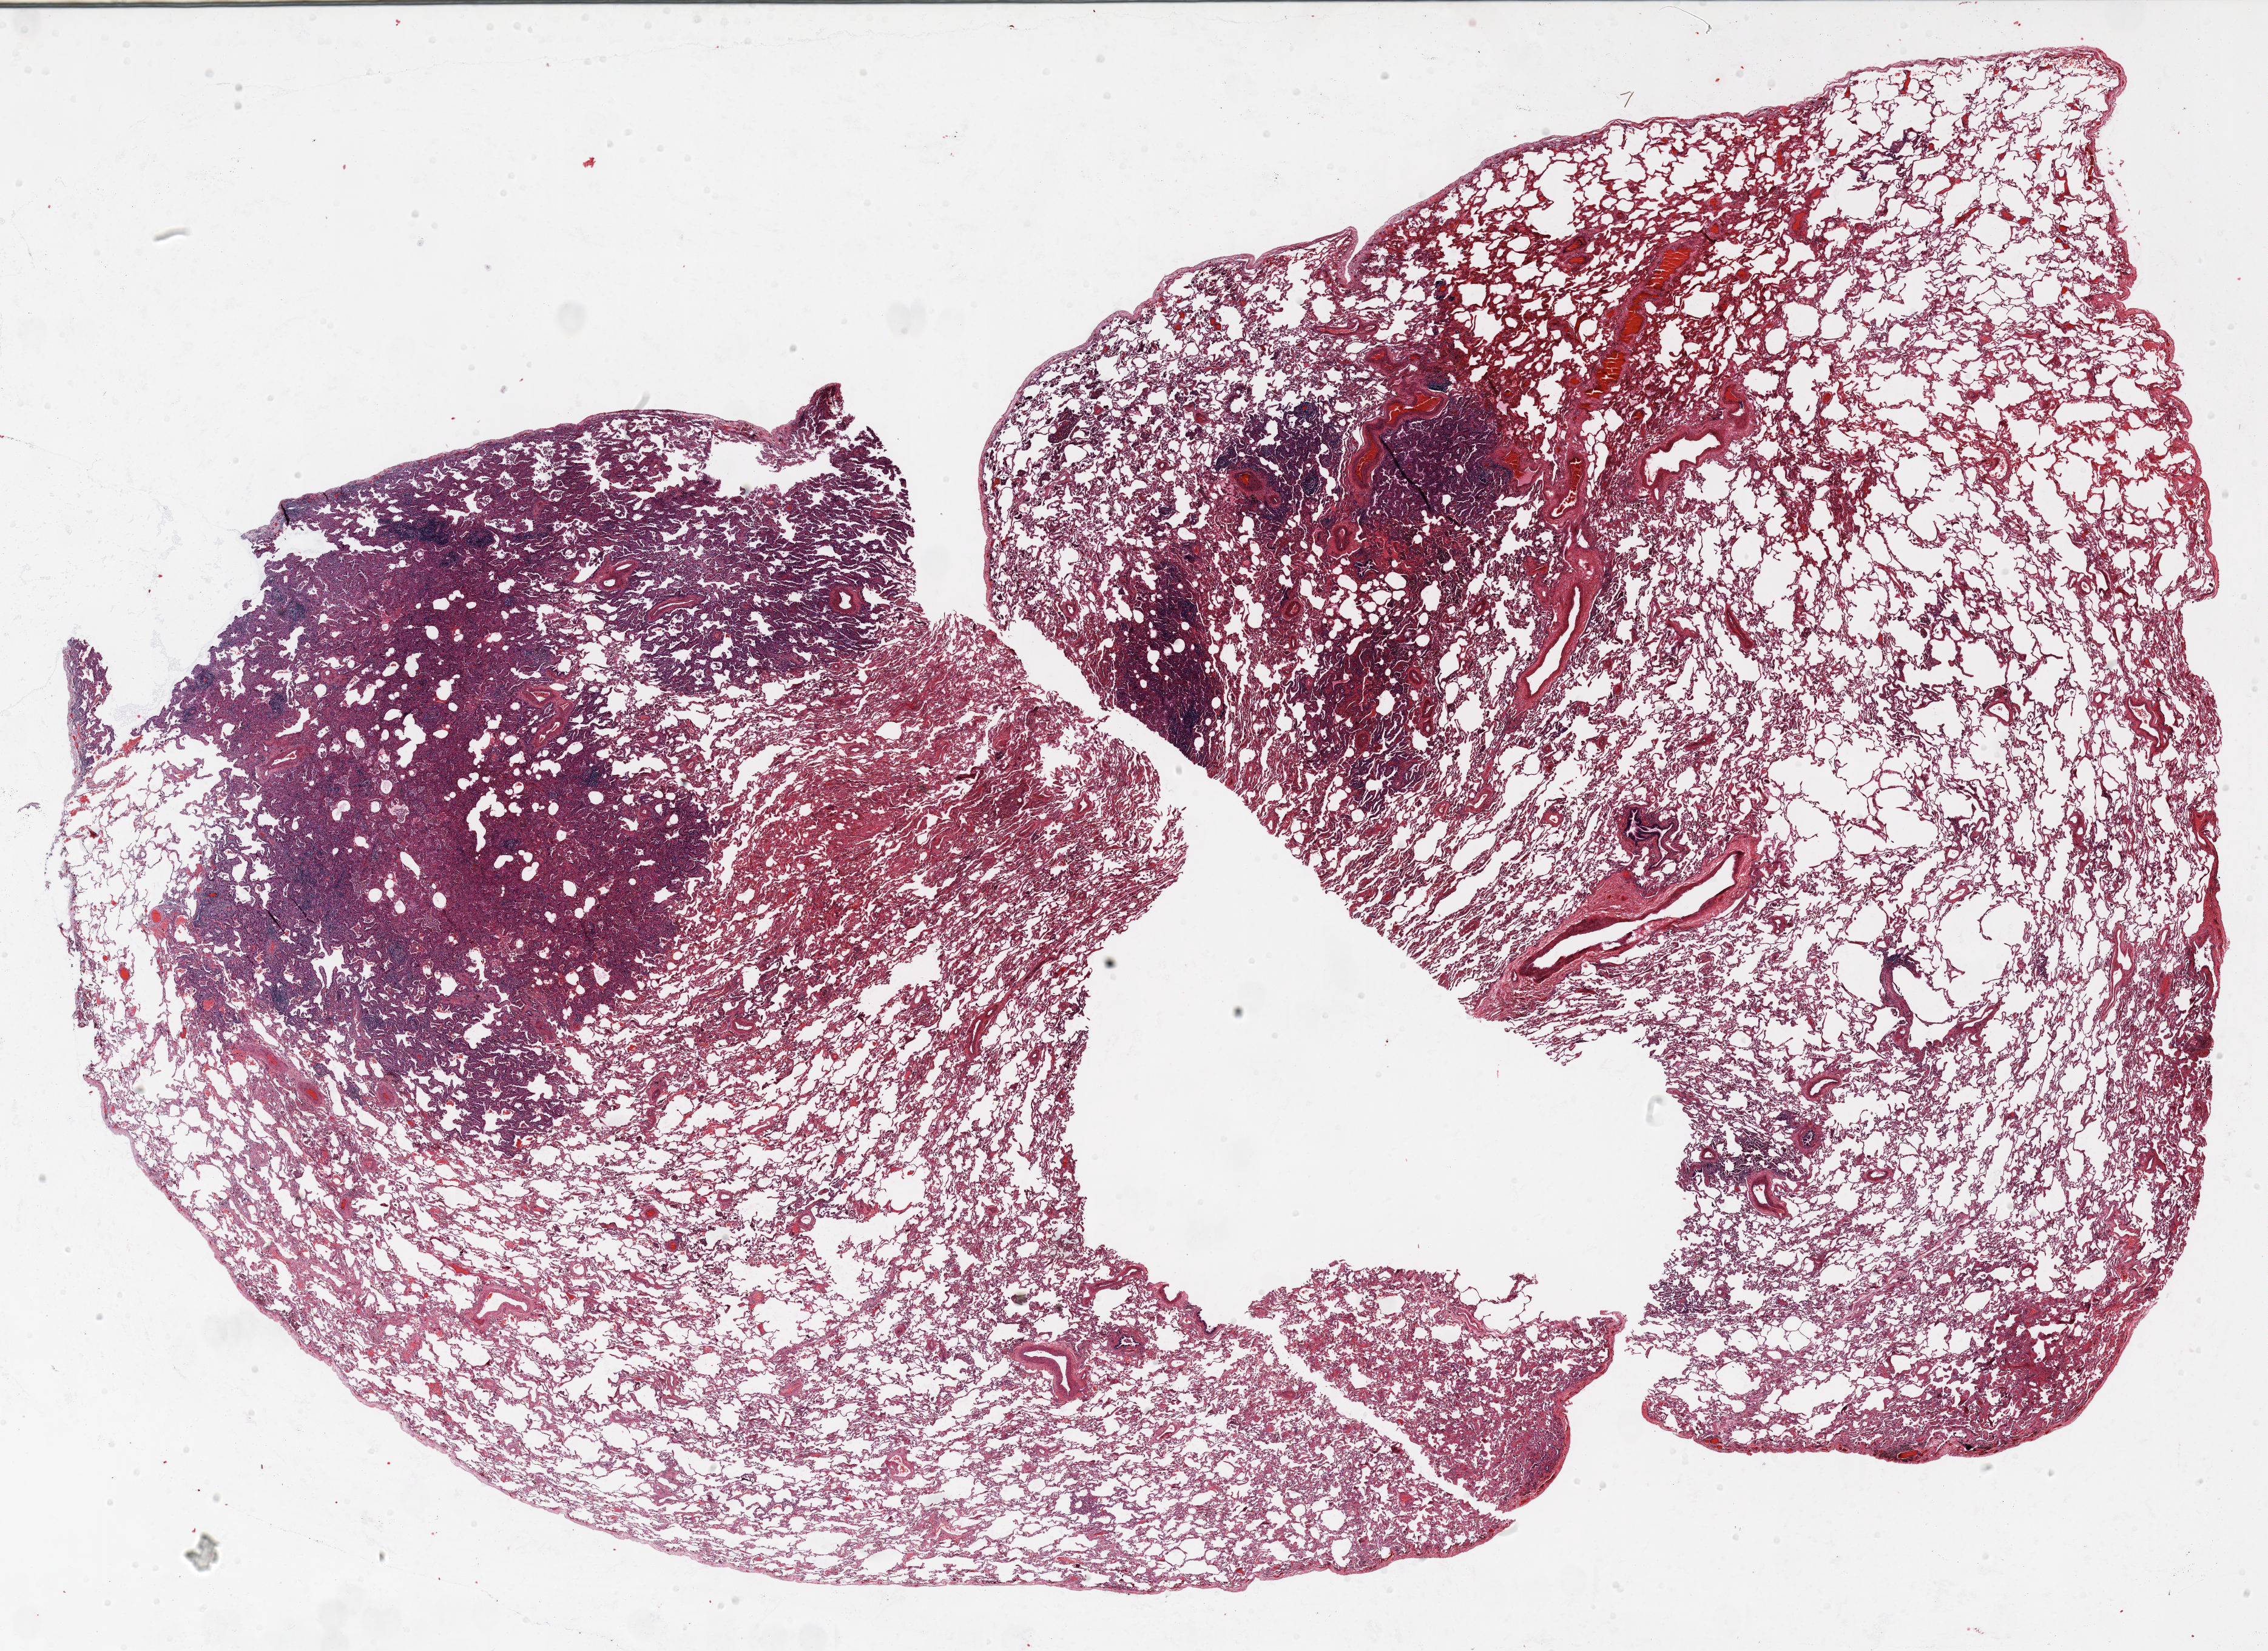
H&E whole-slide image — a low-resolution overview of the entire scanned area, about 30.0 x 21.9 mm (acquisition: 20x scan). Formalin-fixed paraffin-embedded (FFPE) section. Lung tissue. Female patient, aged 56 at enrolment. Current smoker at enrolment. Grade: well differentiated (G1).
Participant's lung-cancer diagnosis: Bronchiolo-alveolar adenocarcinoma, NOS. Tumour size (pathology): 15 mm. Primary tumour location (clinical record): right upper lobe. ICD-O-3 topography: upper lobe of lung (C34.1). Stage (AJCC 6th edition): IA.